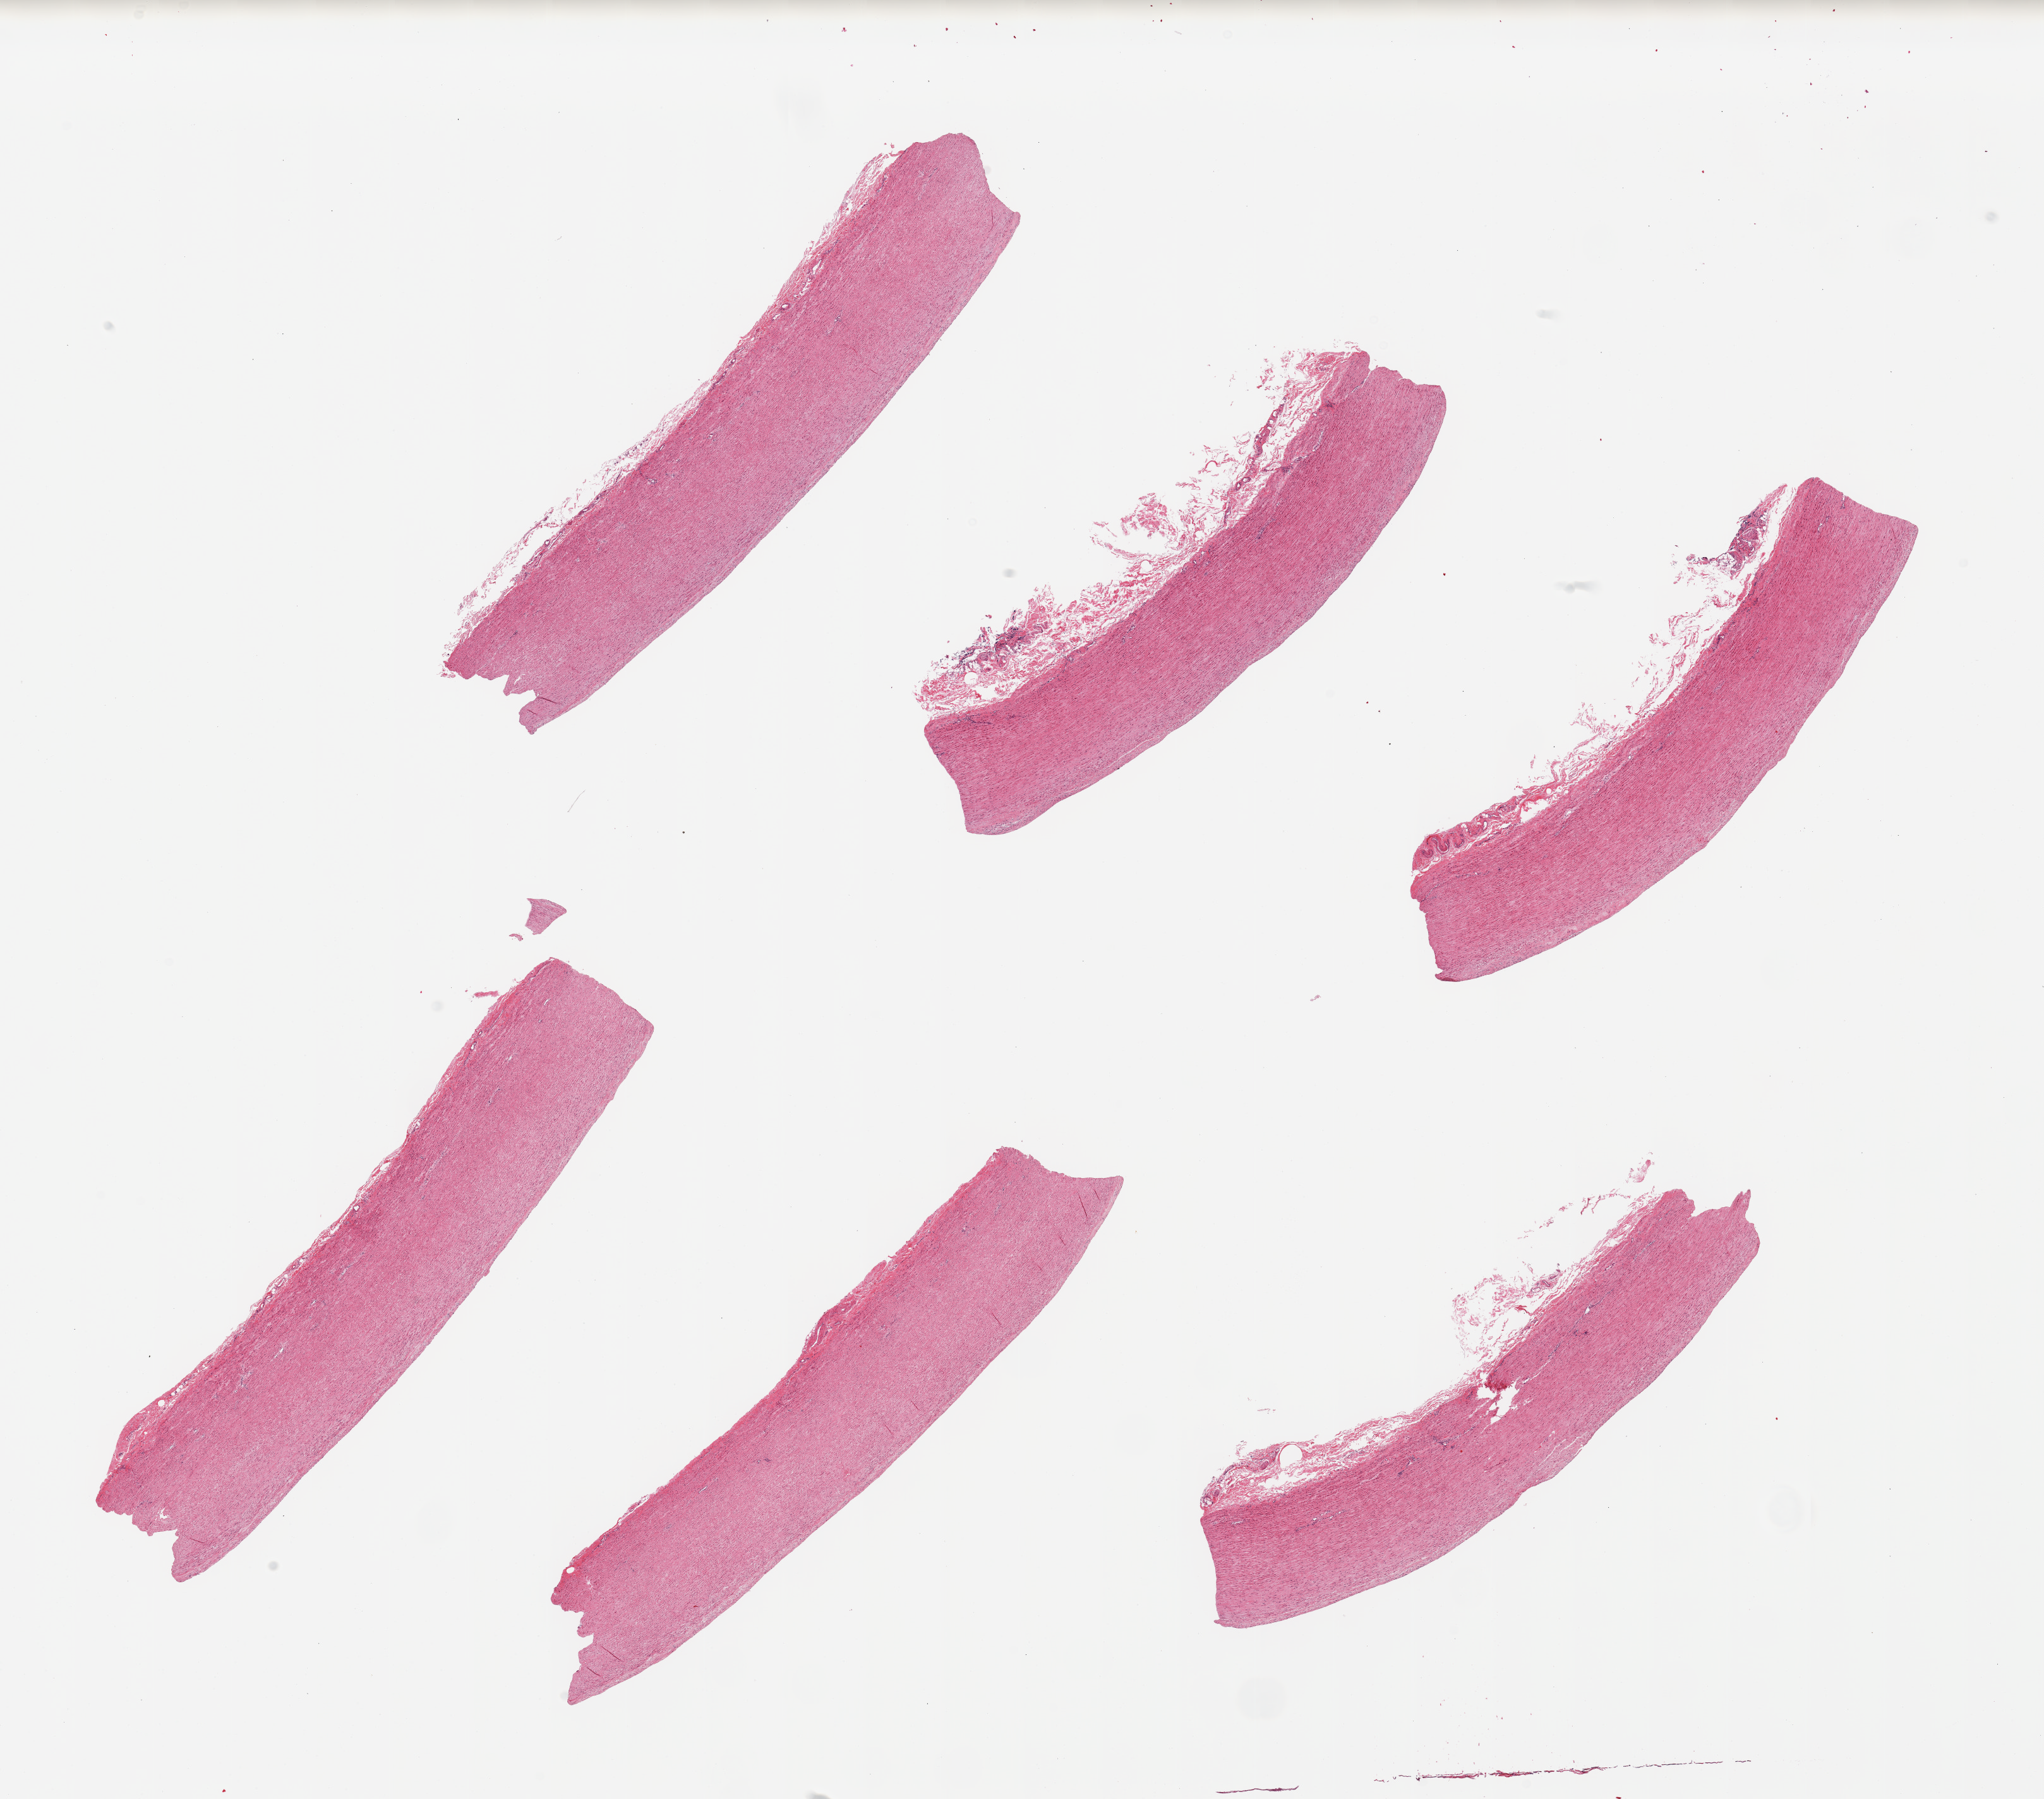
Whole-slide image, H&E stain, brightfield — whole scanned area (about 25.6 x 22.5 mm, slide scanned at 20x) shown as a low-resolution overview; PAXgene-fixed, paraffin-embedded tissue; target tissue: aorta; donor tissue sample. Donor: female.
Review note (as recorded): 6 pieces; trace adherent serosal fat.